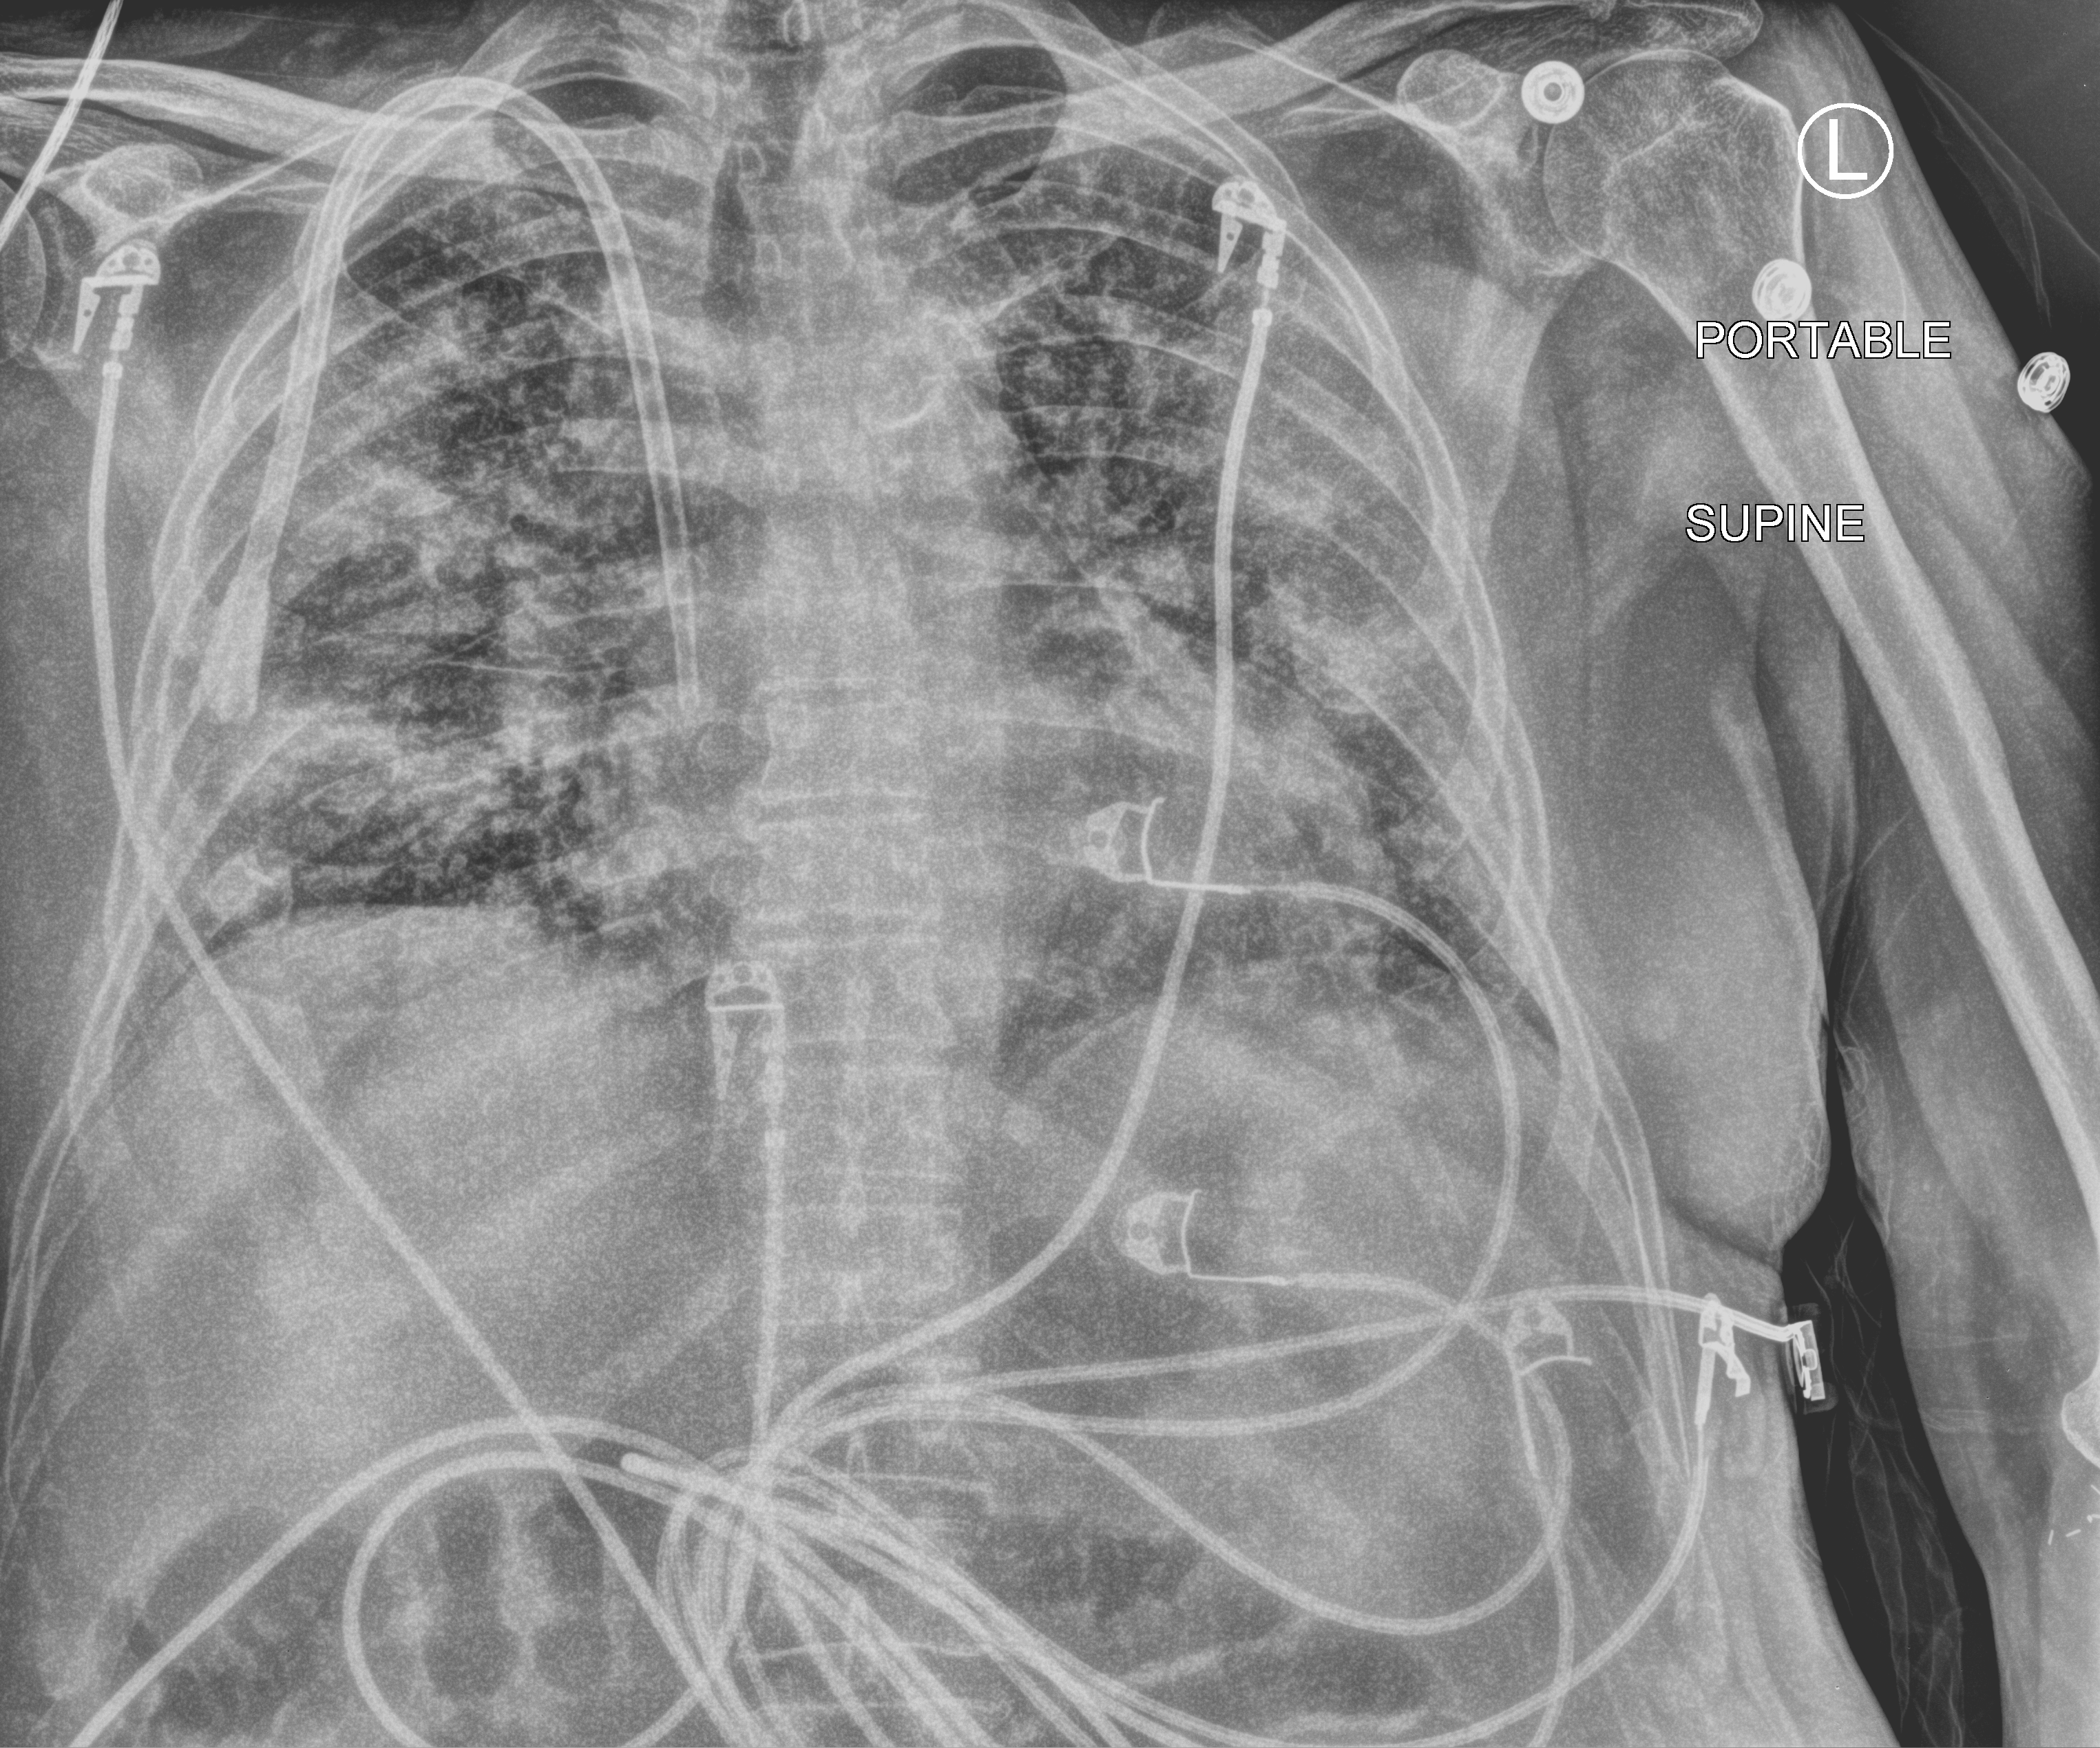
Portable chest radiograph; anteroposterior (AP) projection. Patient hospitalised with COVID-19; male, aged 60–74 years.
From the hospital-stay record, not from the radiograph (when in the stay this image was taken is not recorded): smoking status (admission record): former; admitted to intensive care during this hospital stay: no.